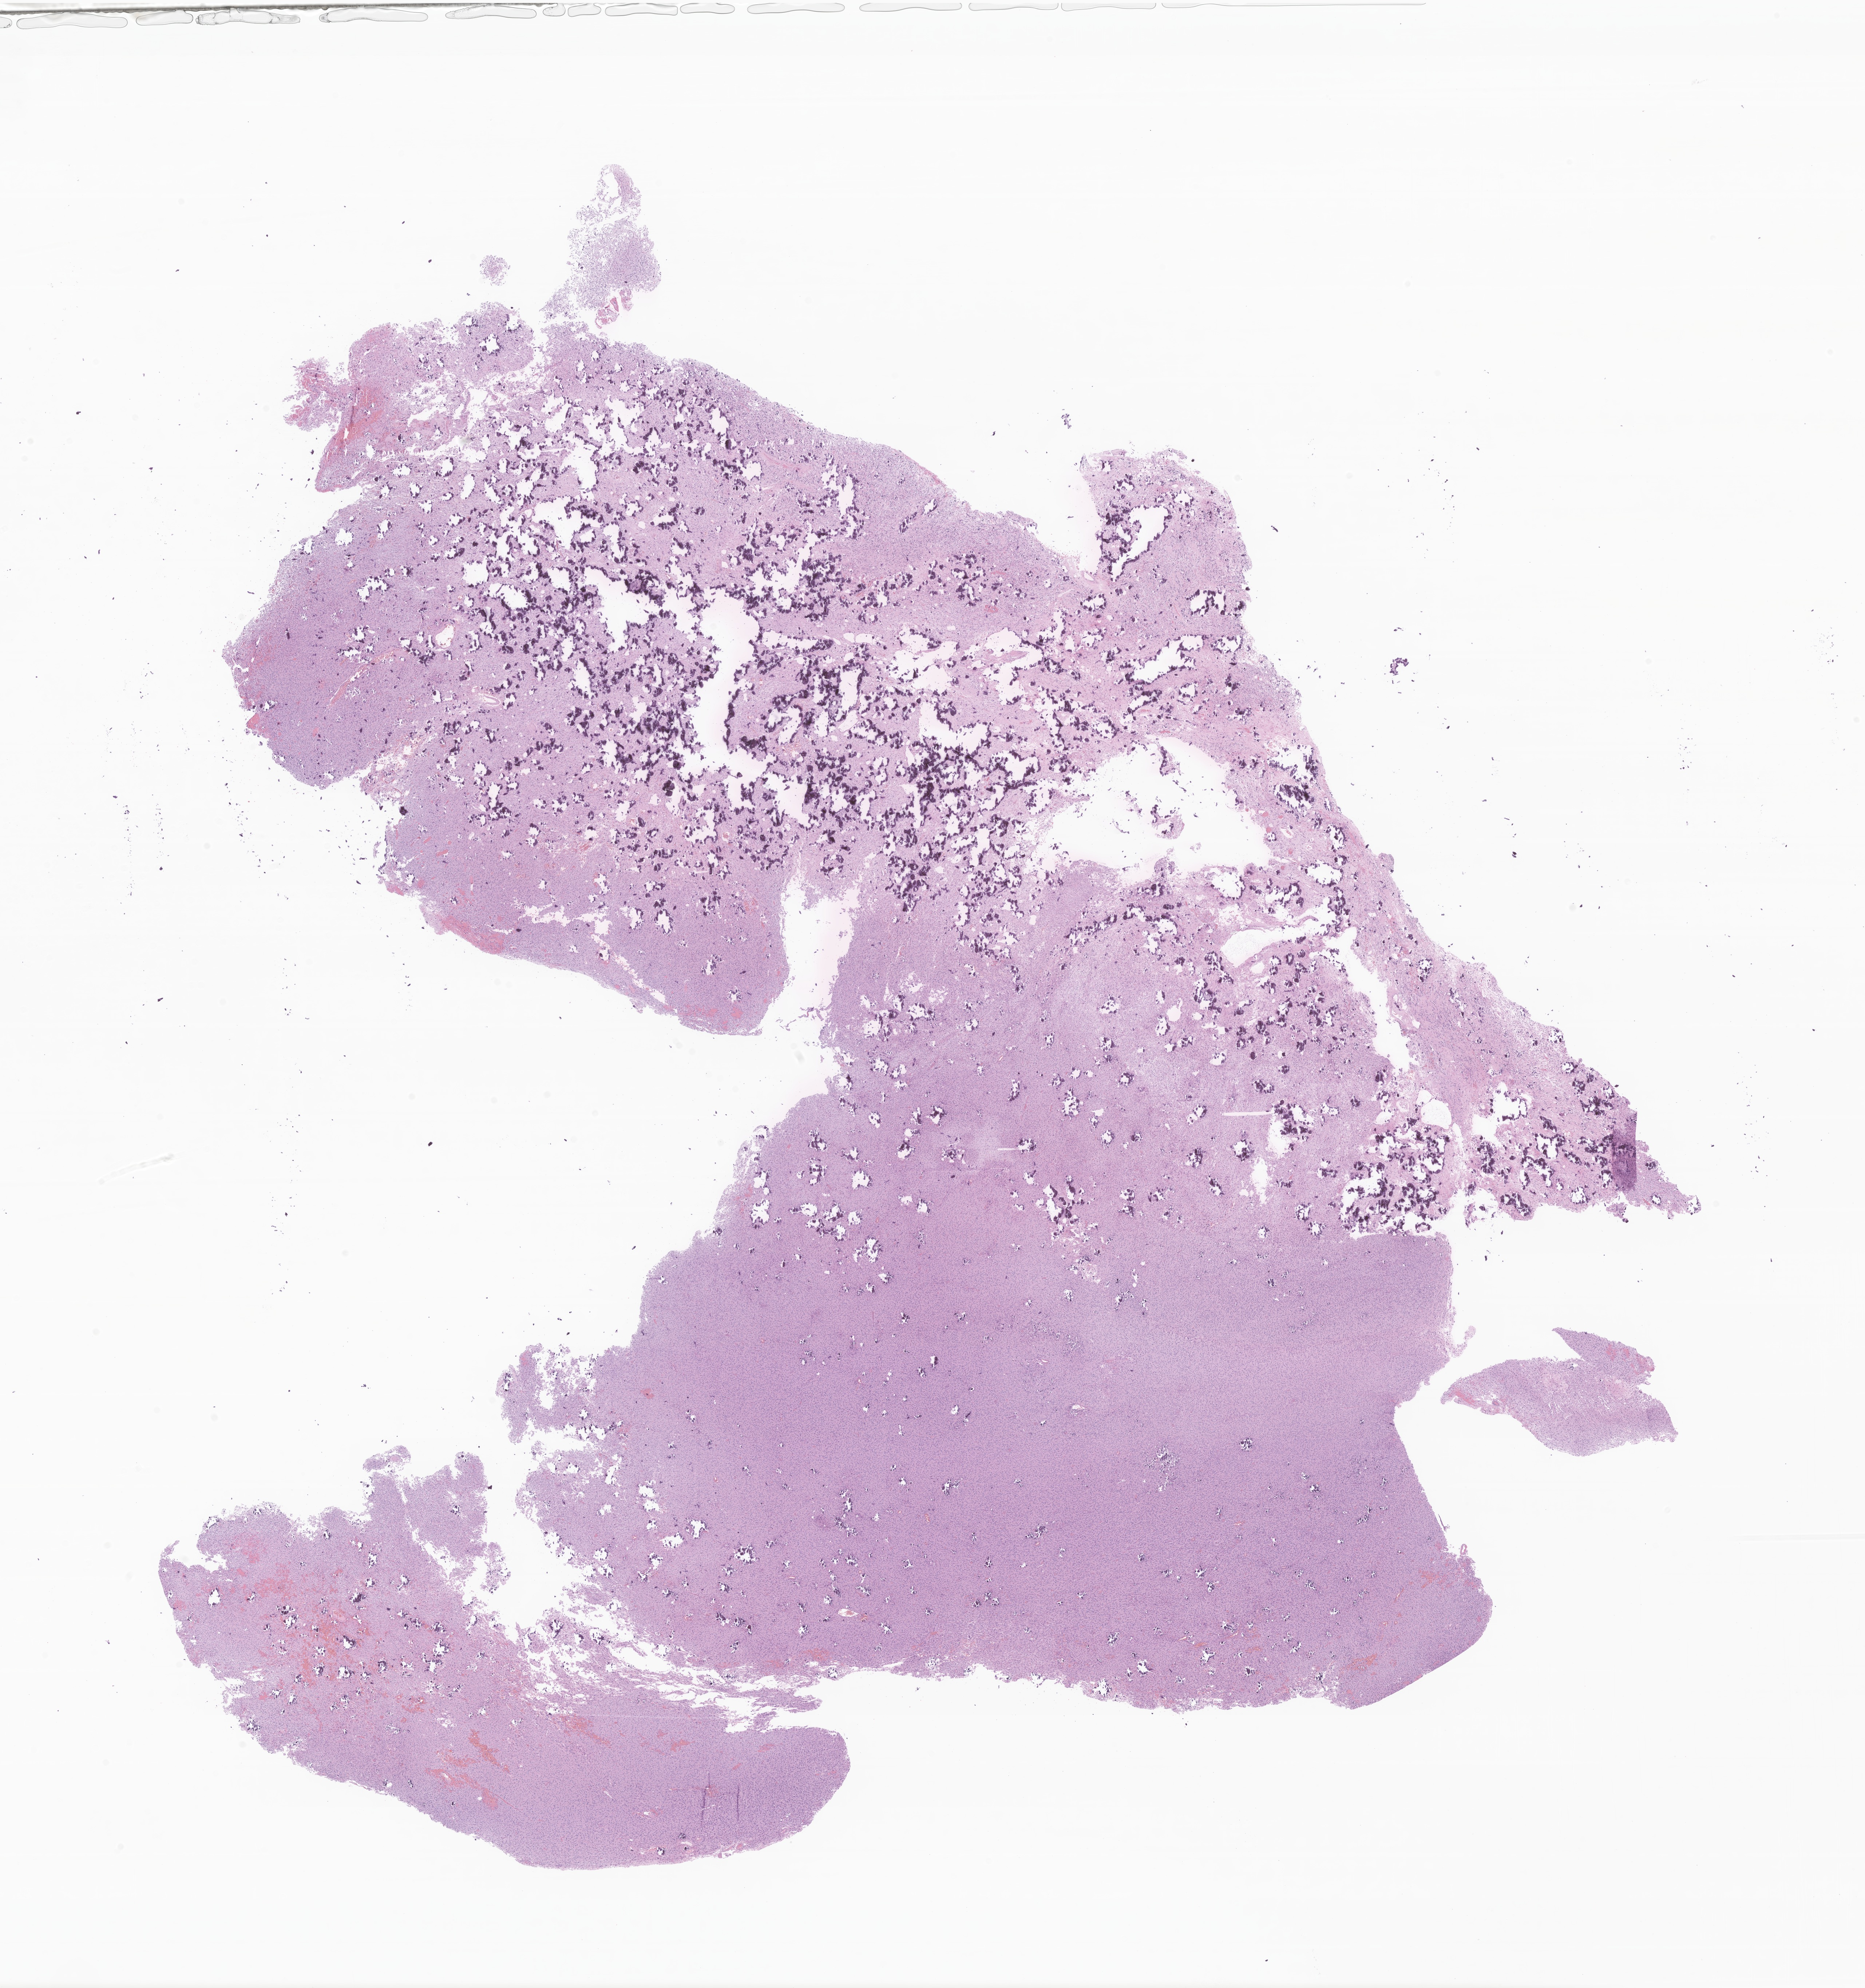
Whole-slide image, hematoxylin and eosin (H&E) stain of tumor tissue from the brain — low-resolution overview of the scanned area, about 21.6 x 23.0 mm. Formalin-fixed paraffin-embedded section. Female patient, age 80 months (6 years 8 months).
Diagnosis (ICD-O-3 morphology term): Neoplasm, uncertain whether benign or malignant.